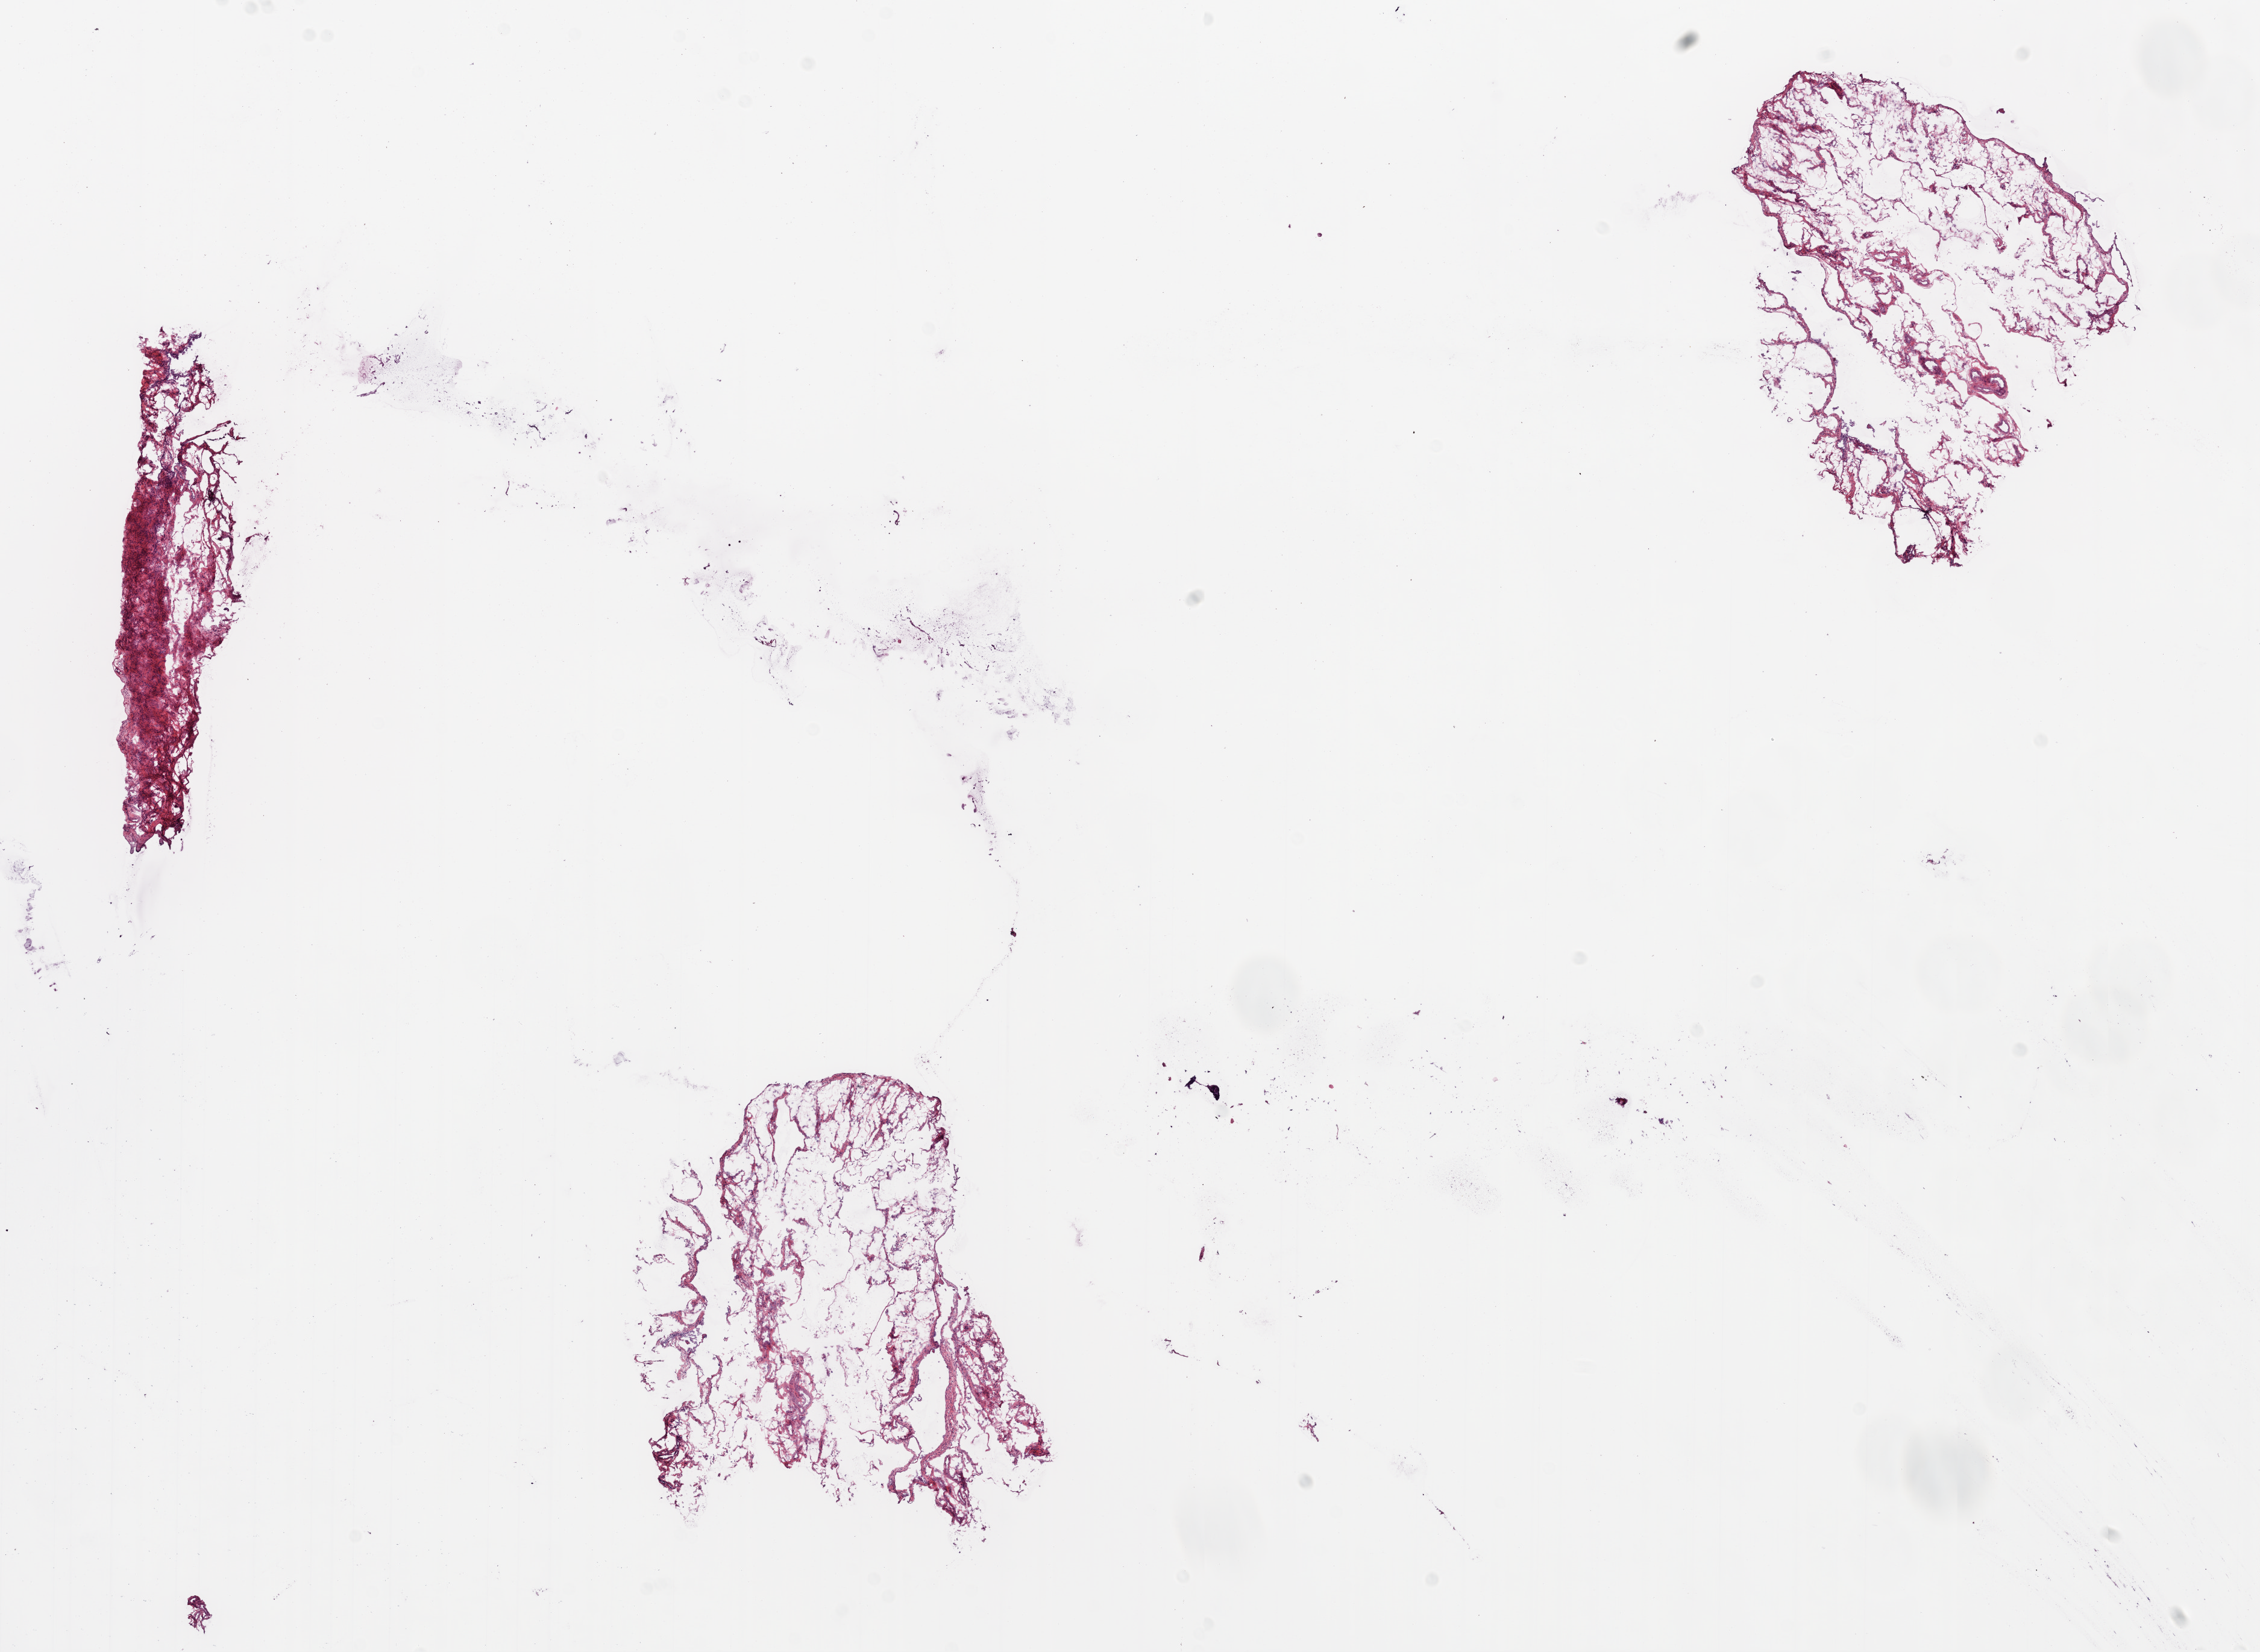
Digitized H&E-stained tissue section (whole slide), shown as a low-resolution overview of the whole scanned area (about 15.0 x 11.0 mm, acquisition: 20x scan); frozen section; ovary, solid tissue normal (non-tumour tissue) sample. Female patient; age at initial diagnosis 59 years.
This section: solid tissue normal sample (biorepository sample class). Patient diagnosis: Serous cystadenocarcinoma, NOS.